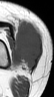
MRI of an extremity soft-tissue mass, one axial slice; slice 22 of 42 in the series (ordered by position); MR volume resampled by the dataset authors to the PET/CT grid (not the native acquisition matrix); 54 × 97 image matrix. Female patient. Case-level facts recorded for this patient, not image findings: histological type: spindle cell suggestive of biphasic synovial sarcoma; grade: intermediate; site of the primary tumour: left knee.
Structures marked on this image (expert contour drawn on MRI and transferred to this co-registered scan by the dataset authors):
- gross tumour volume including surrounding oedema: bounding box (x1, y1, x2, y2) in pixels: (12, 21, 41, 70)
- gross tumour volume (mass): (14, 23, 41, 70)